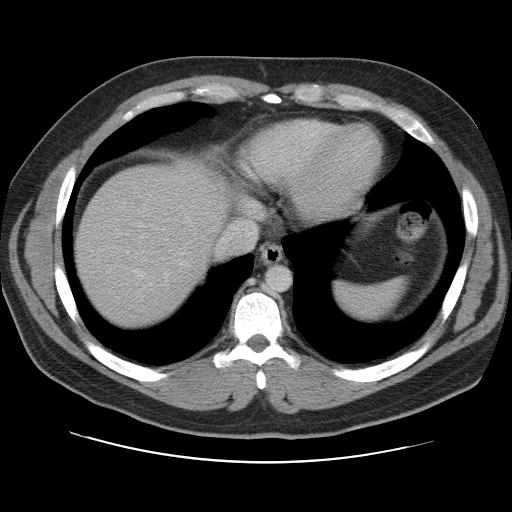
Contrast-enhanced abdominal CT, one axial slice; position 97 of 109 along the scan axis; soft-tissue window (W 400 / L 40 HU); 5 mm slice thickness; 512 × 512 image matrix. Male patient, age 35 years. From the clinical record (not read from this slice): diagnosis: colorectal cancer liver metastases, imaged before liver resection; multiple liver metastases: yes; largest metastasis: 2.8 cm; disease in both lobes: yes.
Structures marked on this image (expert manual segmentation):
- hepatic veins: bounding box [x1, y1, x2, y2] px = [134, 223, 256, 279]
- liver: [75, 166, 229, 328]
- planned liver remnant (the part of the liver to remain after resection): [74, 166, 230, 328]